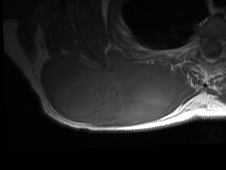
MRI of an extremity soft-tissue mass, one axial slice; slice 33 of 81 in the series (ordered by position); MR volume resampled by the dataset authors to the PET/CT grid (not the native acquisition matrix); 3.27 mm slice thickness; 226 × 170 image matrix, field of view 221 × 166 mm. Male patient. Case-level facts recorded for this patient, not image findings: histological type: pleiomorphic spindle cell undifferentiated; grade: high; site of the primary tumour: right parascapusular.
Annotated regions visible in this slice (expert contour drawn on MRI and transferred to this co-registered scan by the dataset authors):
- gross tumour volume including surrounding oedema: bounding box <42,49,196,128> (left, top, right, bottom; pixels)
- gross tumour volume (mass): <42,49,177,125>